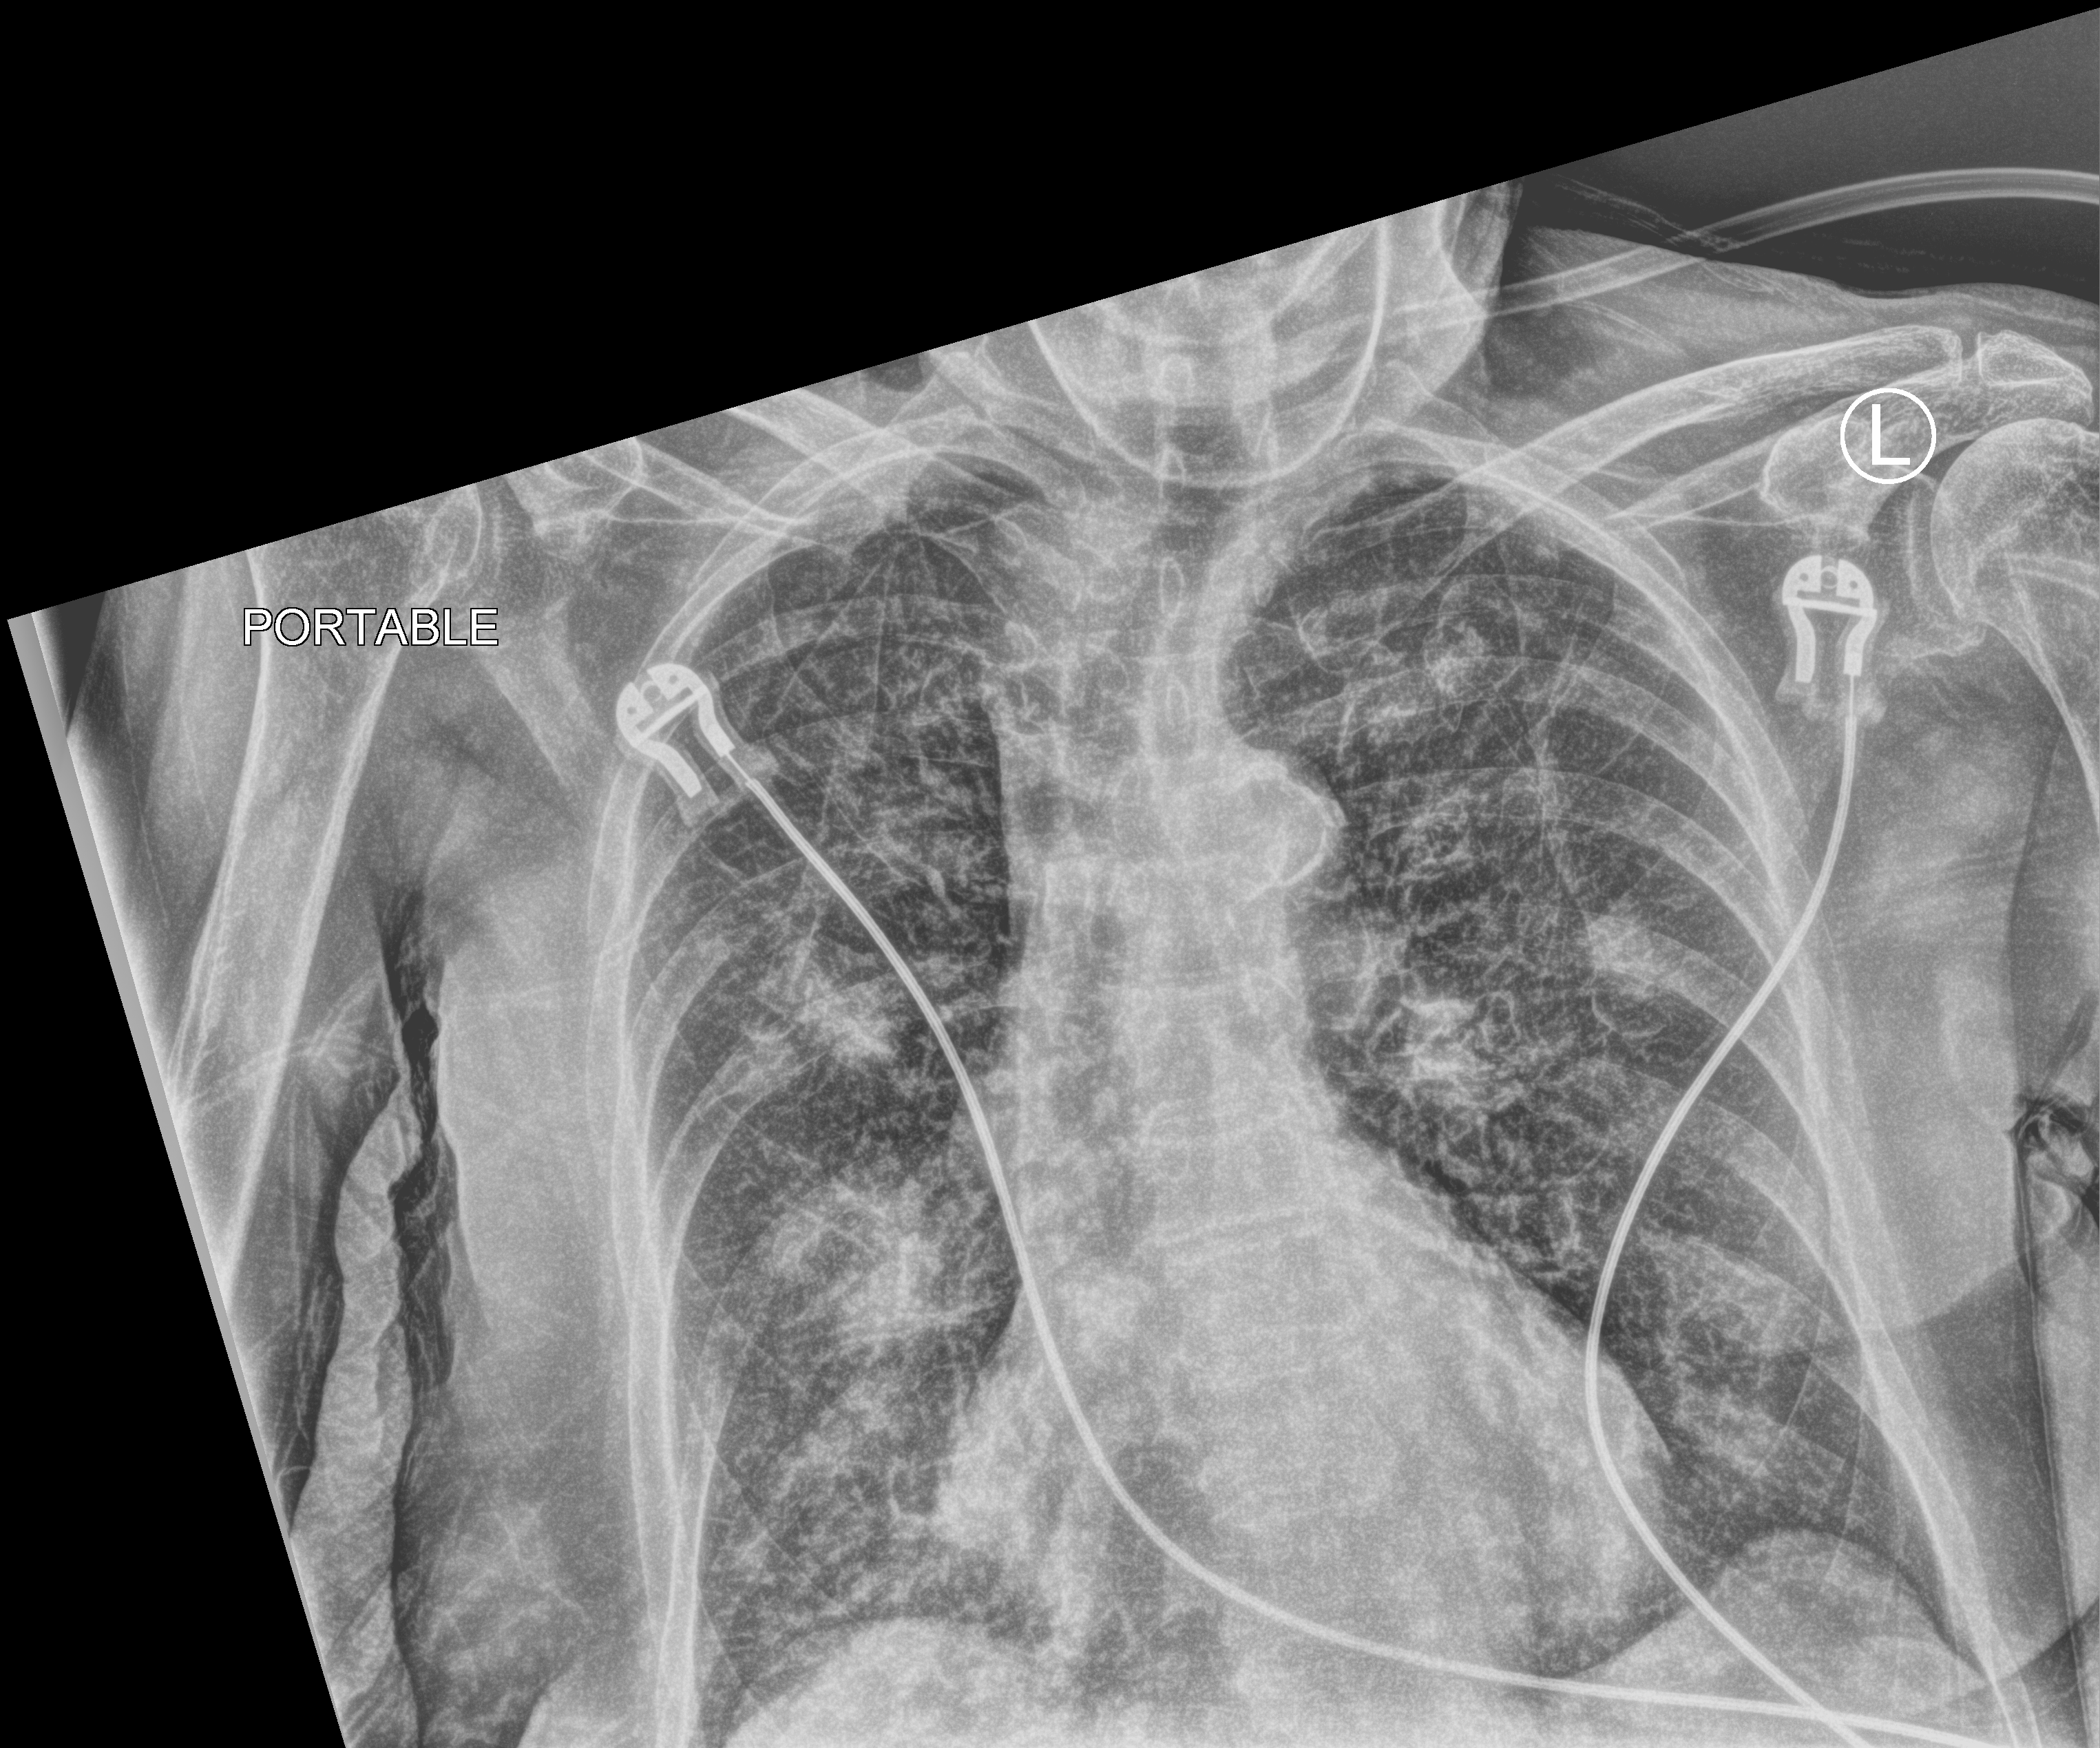
Chest X-ray (portable), anteroposterior (AP) projection. Patient hospitalised with COVID-19; female, aged 75–90 years.
From the hospital-stay record, not from the radiograph (when in the stay this image was taken is not recorded):
- admitted to intensive care during this hospital stay: no
- mechanically ventilated during this hospital stay: no
- length of hospital stay: 2 days